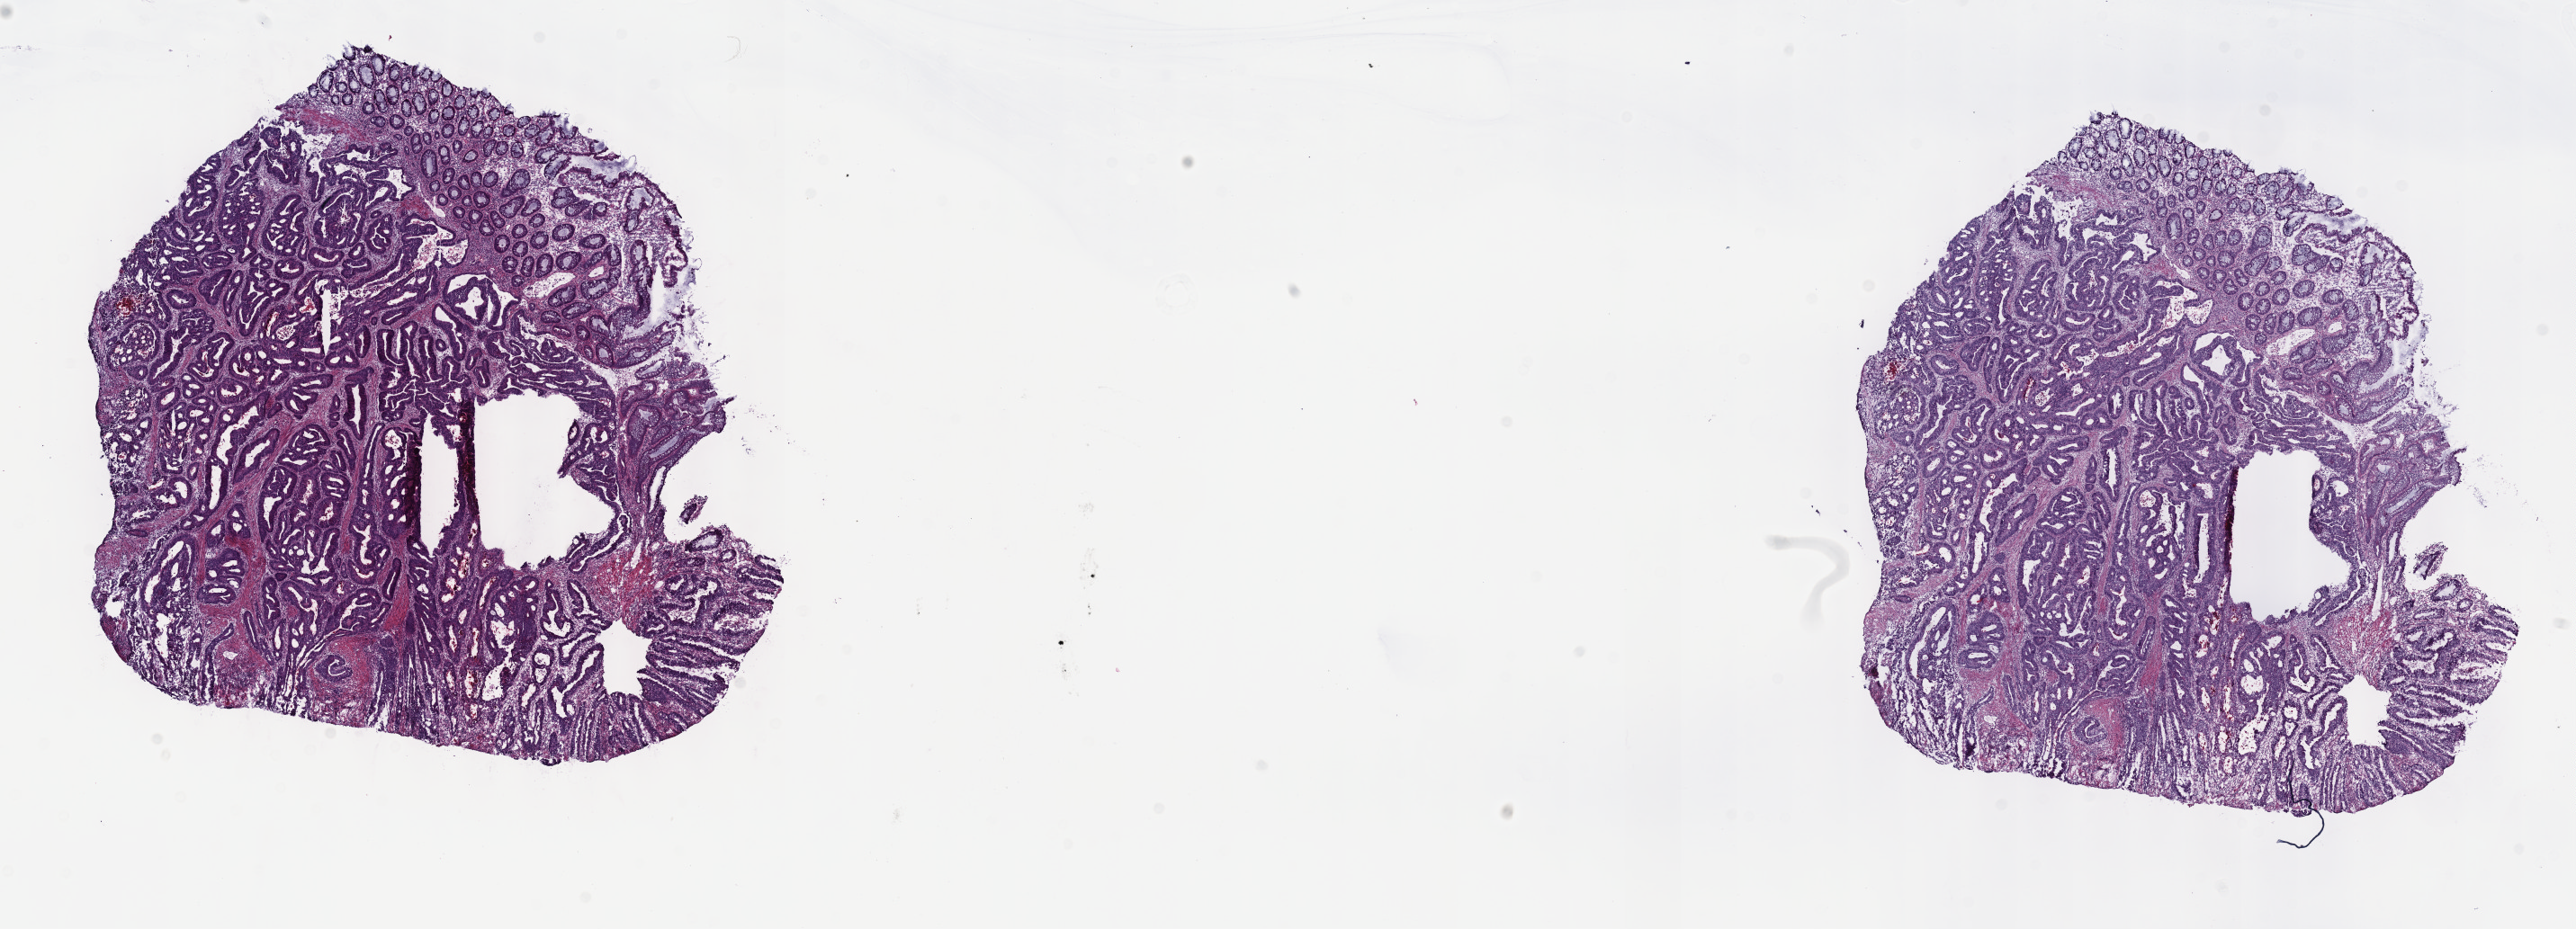
Digitized H&E tissue section (whole slide) — whole scanned area (about 23.2 x 8.4 mm) shown as a low-resolution overview. Frozen section from the top of the tissue portion. Primary tumour sample from the colon. Patient: male, age at initial diagnosis 44 years. Slide review estimates, as recorded: tumour cells 75%, tumour nuclei 75%, normal cells 15%, stromal cells 7%, necrosis 3%. Inflammatory infiltration, as recorded: lymphocyte infiltration 5%, monocyte infiltration 2%, neutrophil infiltration 2%.
- AJCC pathologic stage: IVA (7th edition)
- lymph nodes positive (case pathology): 6 of 24 examined
- pathologic diagnosis: Adenocarcinoma, NOS (sigmoid colon)